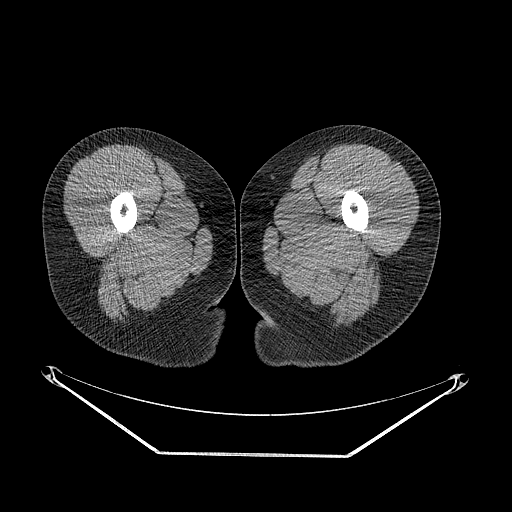
CT of an extremity soft-tissue mass (from a PET/CT study), one axial slice; position 14 of 267 along the scan axis; reconstruction kernel STANDARD; 120 kVp; soft-tissue window (W 400 / L 40 HU); 3.75 mm slice thickness; 512 × 512 image matrix, field of view 500 × 500 mm. Female patient. Case-level facts recorded for this patient, not image findings: histological type: epithelioid sarcoma; grade: intermediate; site of the primary tumour: right buttock.
Annotated regions visible in this slice (expert contour drawn on MRI and transferred to this co-registered scan by the dataset authors):
- gross tumour volume including surrounding oedema: bounding box <192,331,222,371> (left, top, right, bottom; pixels)